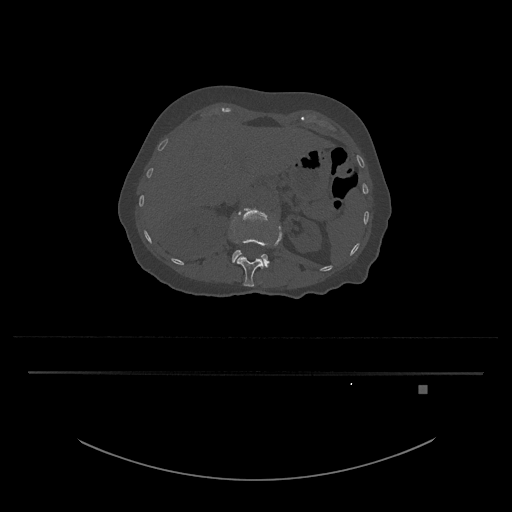
CT including the spine, one axial slice; position 532 of 797 along the scan axis; reconstruction kernel Br40s/3; 120 kVp; bone window (W 1800 / L 400 HU); 0.5 mm slice thickness; 512 × 512 image matrix. Female patient, age 57 years. Case-level facts recorded for this patient, not image findings: primary cancer: cervical.
Annotated regions visible in this slice (semi-automatically segmented with operator editing):
- L1 vertebra: bounding box <232,226,282,287> (left, top, right, bottom; pixels)